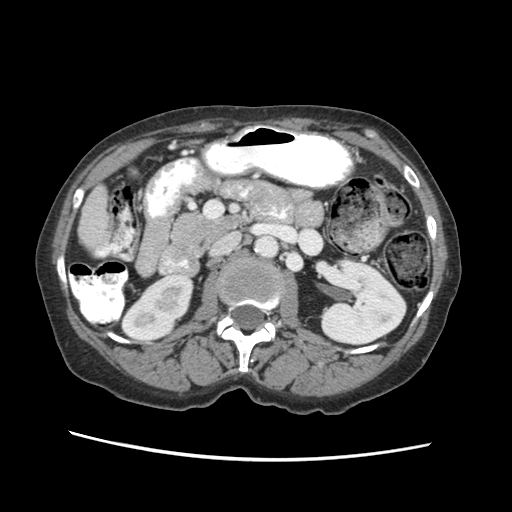
Contrast-enhanced abdominal CT (liver protocol), one axial slice. Reconstruction kernel STANDARD. Soft-tissue window (W 400 / L 40 HU). 2.5 mm slice thickness. 512 × 512 image matrix. From the clinical record (not read from this slice): diagnosis: hepatocellular carcinoma (patient treated with transarterial chemoembolisation; whether this scan precedes or follows treatment is not stated here); TNM stage (as recorded): Stage-I; Child-Pugh class: B.
Annotated regions visible in this slice (semi-automatically segmented with operator editing):
- liver parenchyma outside the tumour (the mass and vessels are separate outlines, so this box may not span the whole liver): bounding box <78,182,110,248> (left, top, right, bottom; pixels)